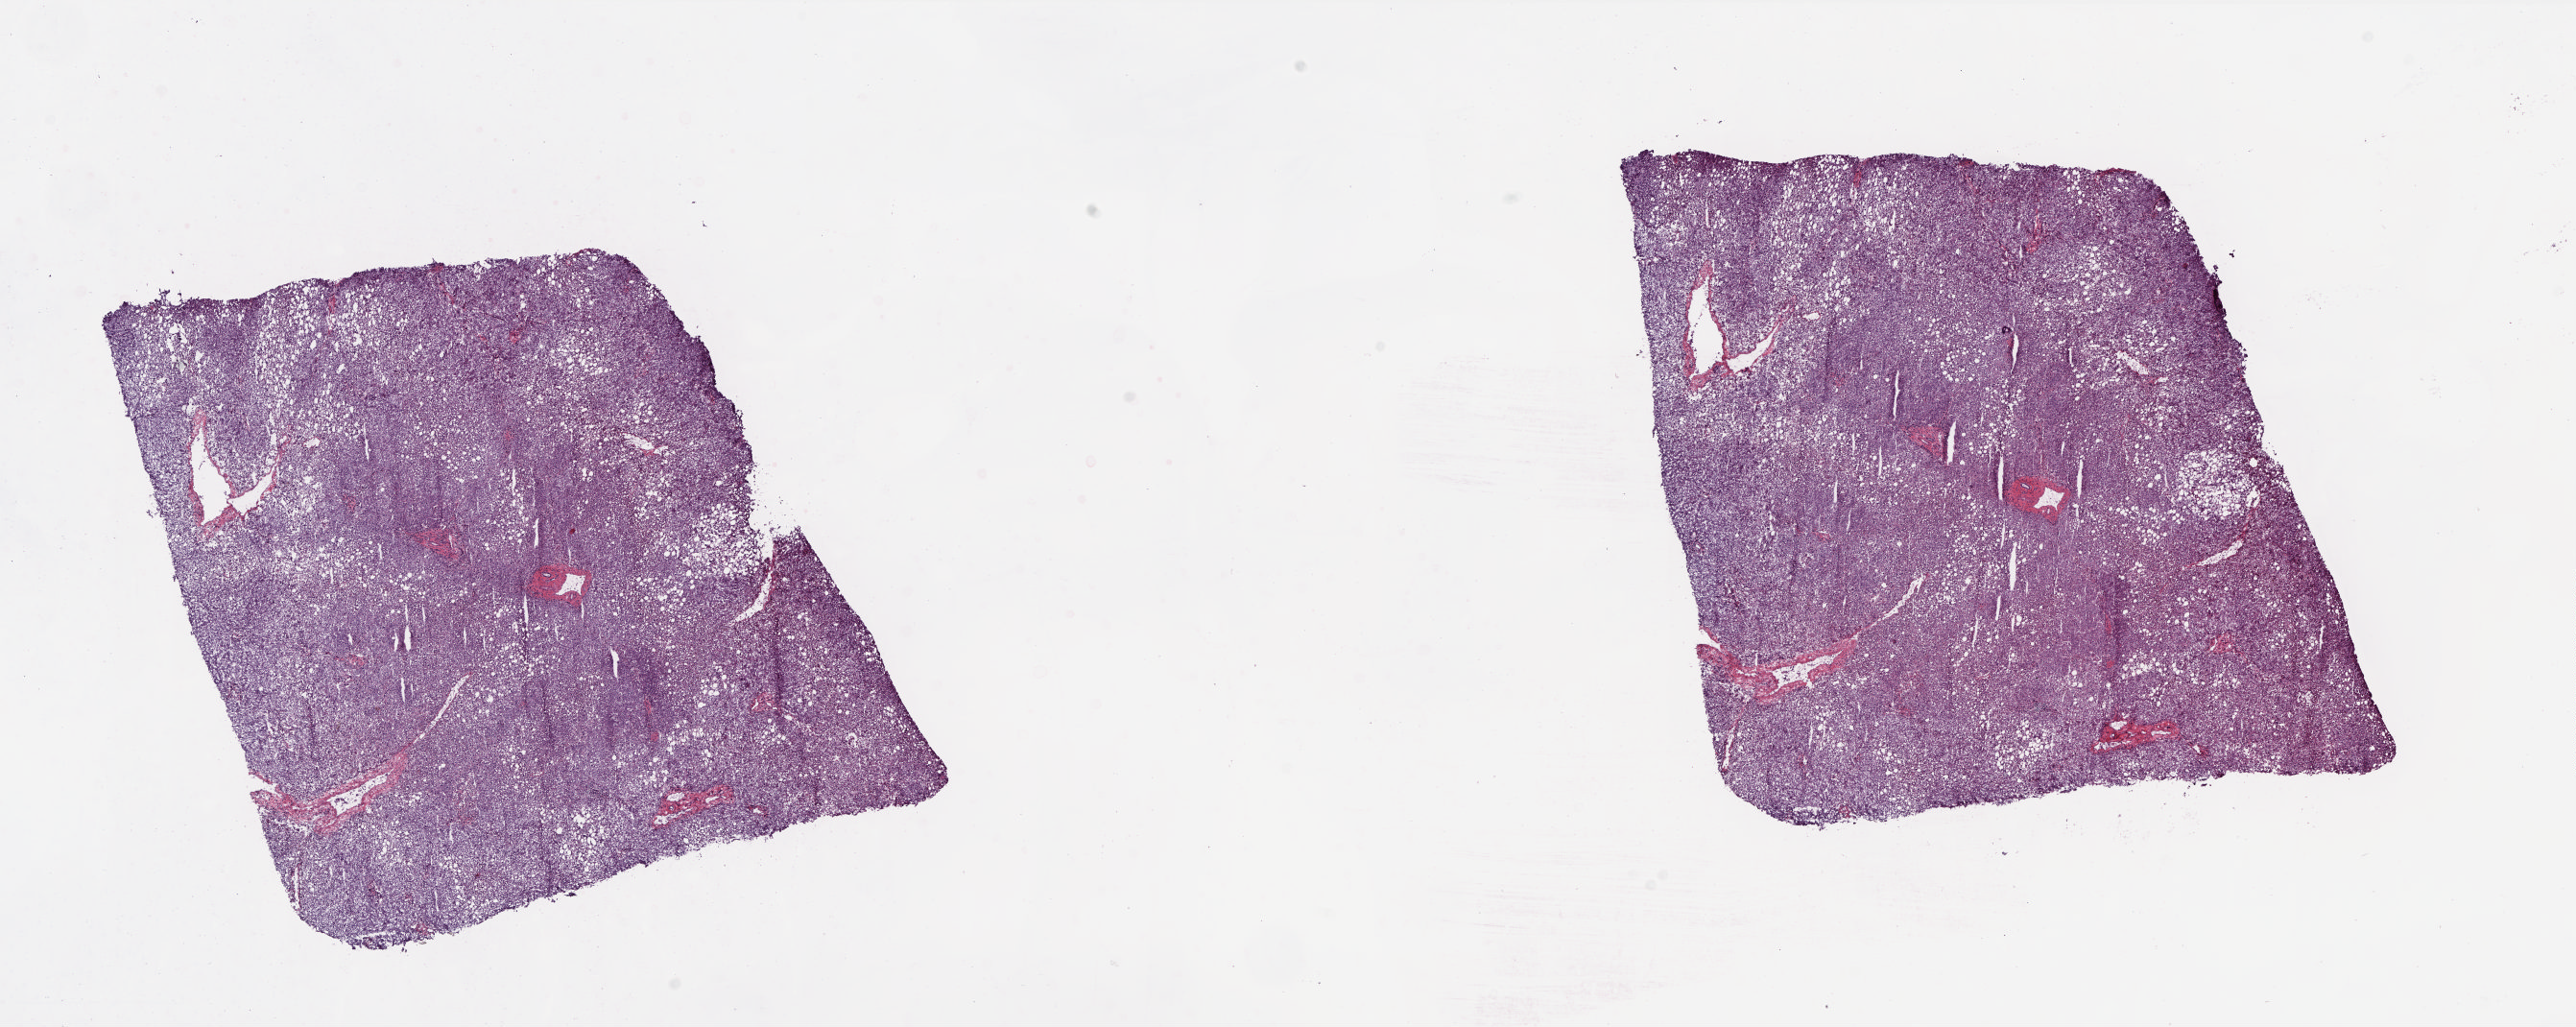
H&E-stained whole-slide image, low-resolution overview of the scanned area, about 21.6 x 8.6 mm (from a 20x scan), frozen section from the top of the tissue portion, sample: solid tissue normal (non-tumour tissue), liver. Patient: female, age at initial diagnosis 56 years. Slide review estimates, as recorded: tumour cells 0%, tumour nuclei 0%, normal cells 100%, stromal cells 0%, necrosis 0%. Inflammatory infiltration, as recorded: lymphocyte infiltration 3%, monocyte infiltration 0%, neutrophil infiltration 1%.
* this section: solid tissue normal sample (biorepository sample class)
* patient diagnosis: Hepatocellular carcinoma, NOS